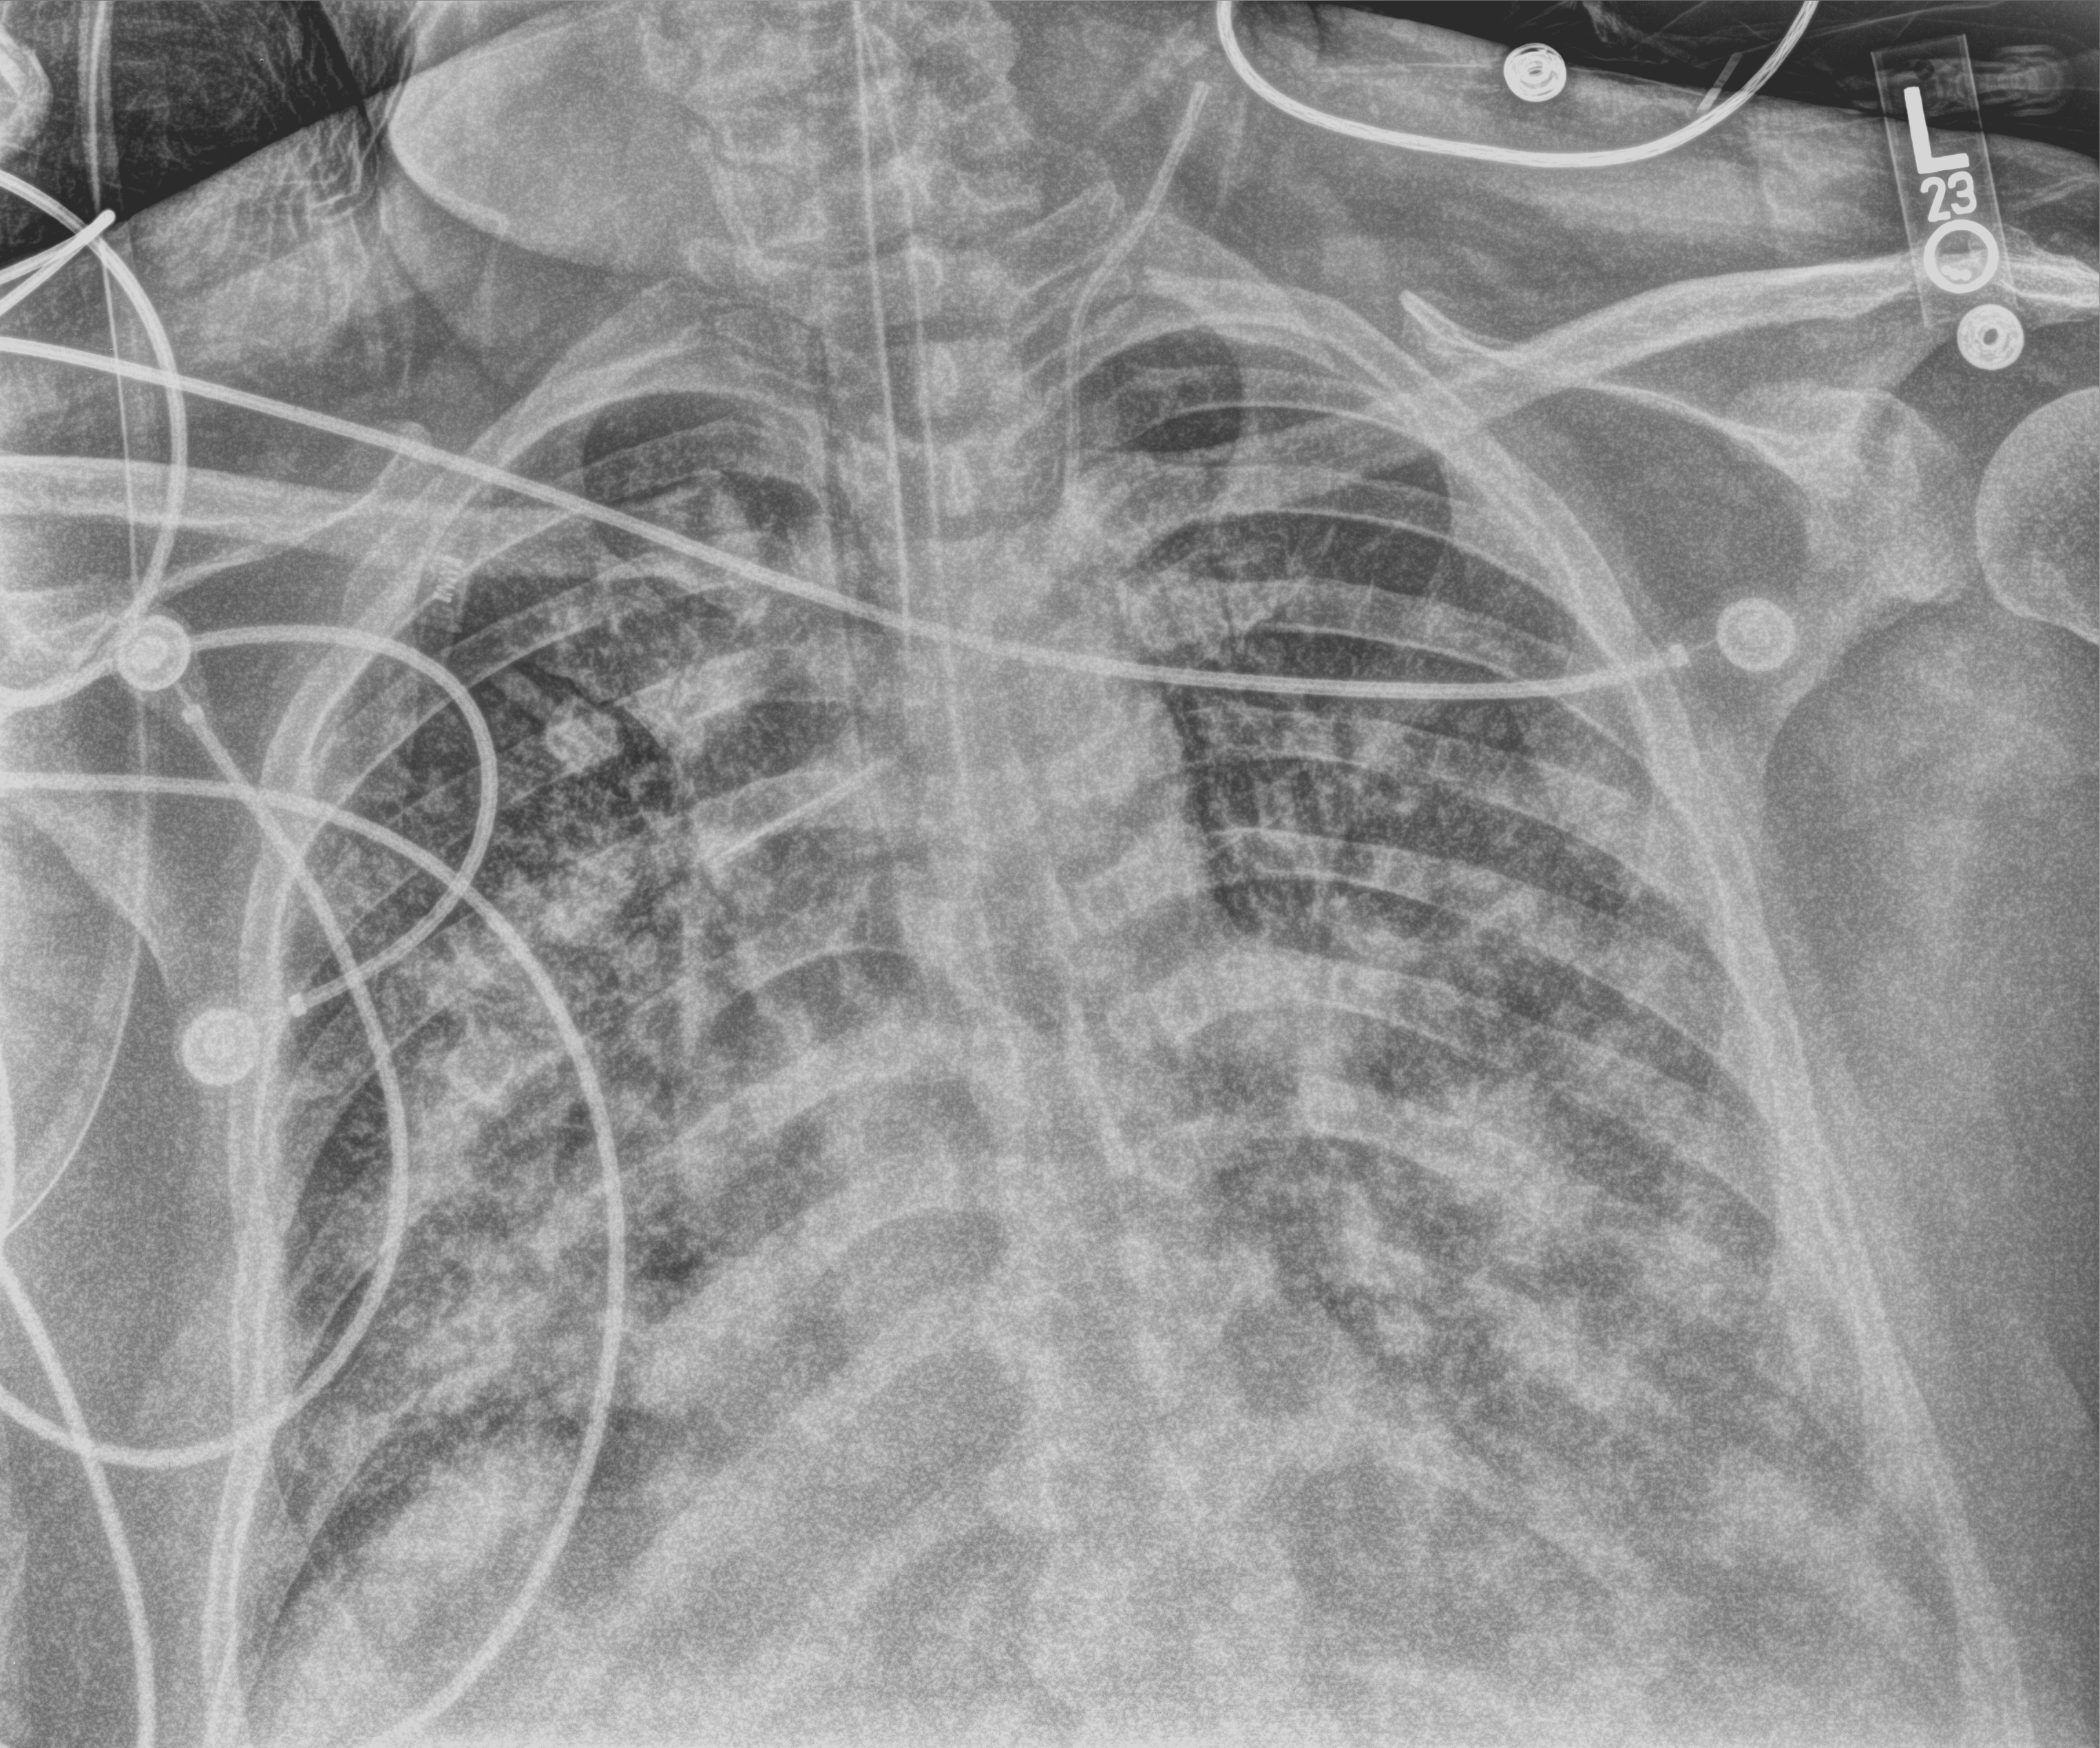
Bedside chest radiograph (computed radiography); anteroposterior (AP) projection. Adult patient hospitalised with COVID-19, age 18–59 years.
Hospital-stay facts (about this admission, not read from this image; timing relative to this image not recorded): mechanically ventilated during this hospital stay: yes; chronic kidney disease (admission record): no.